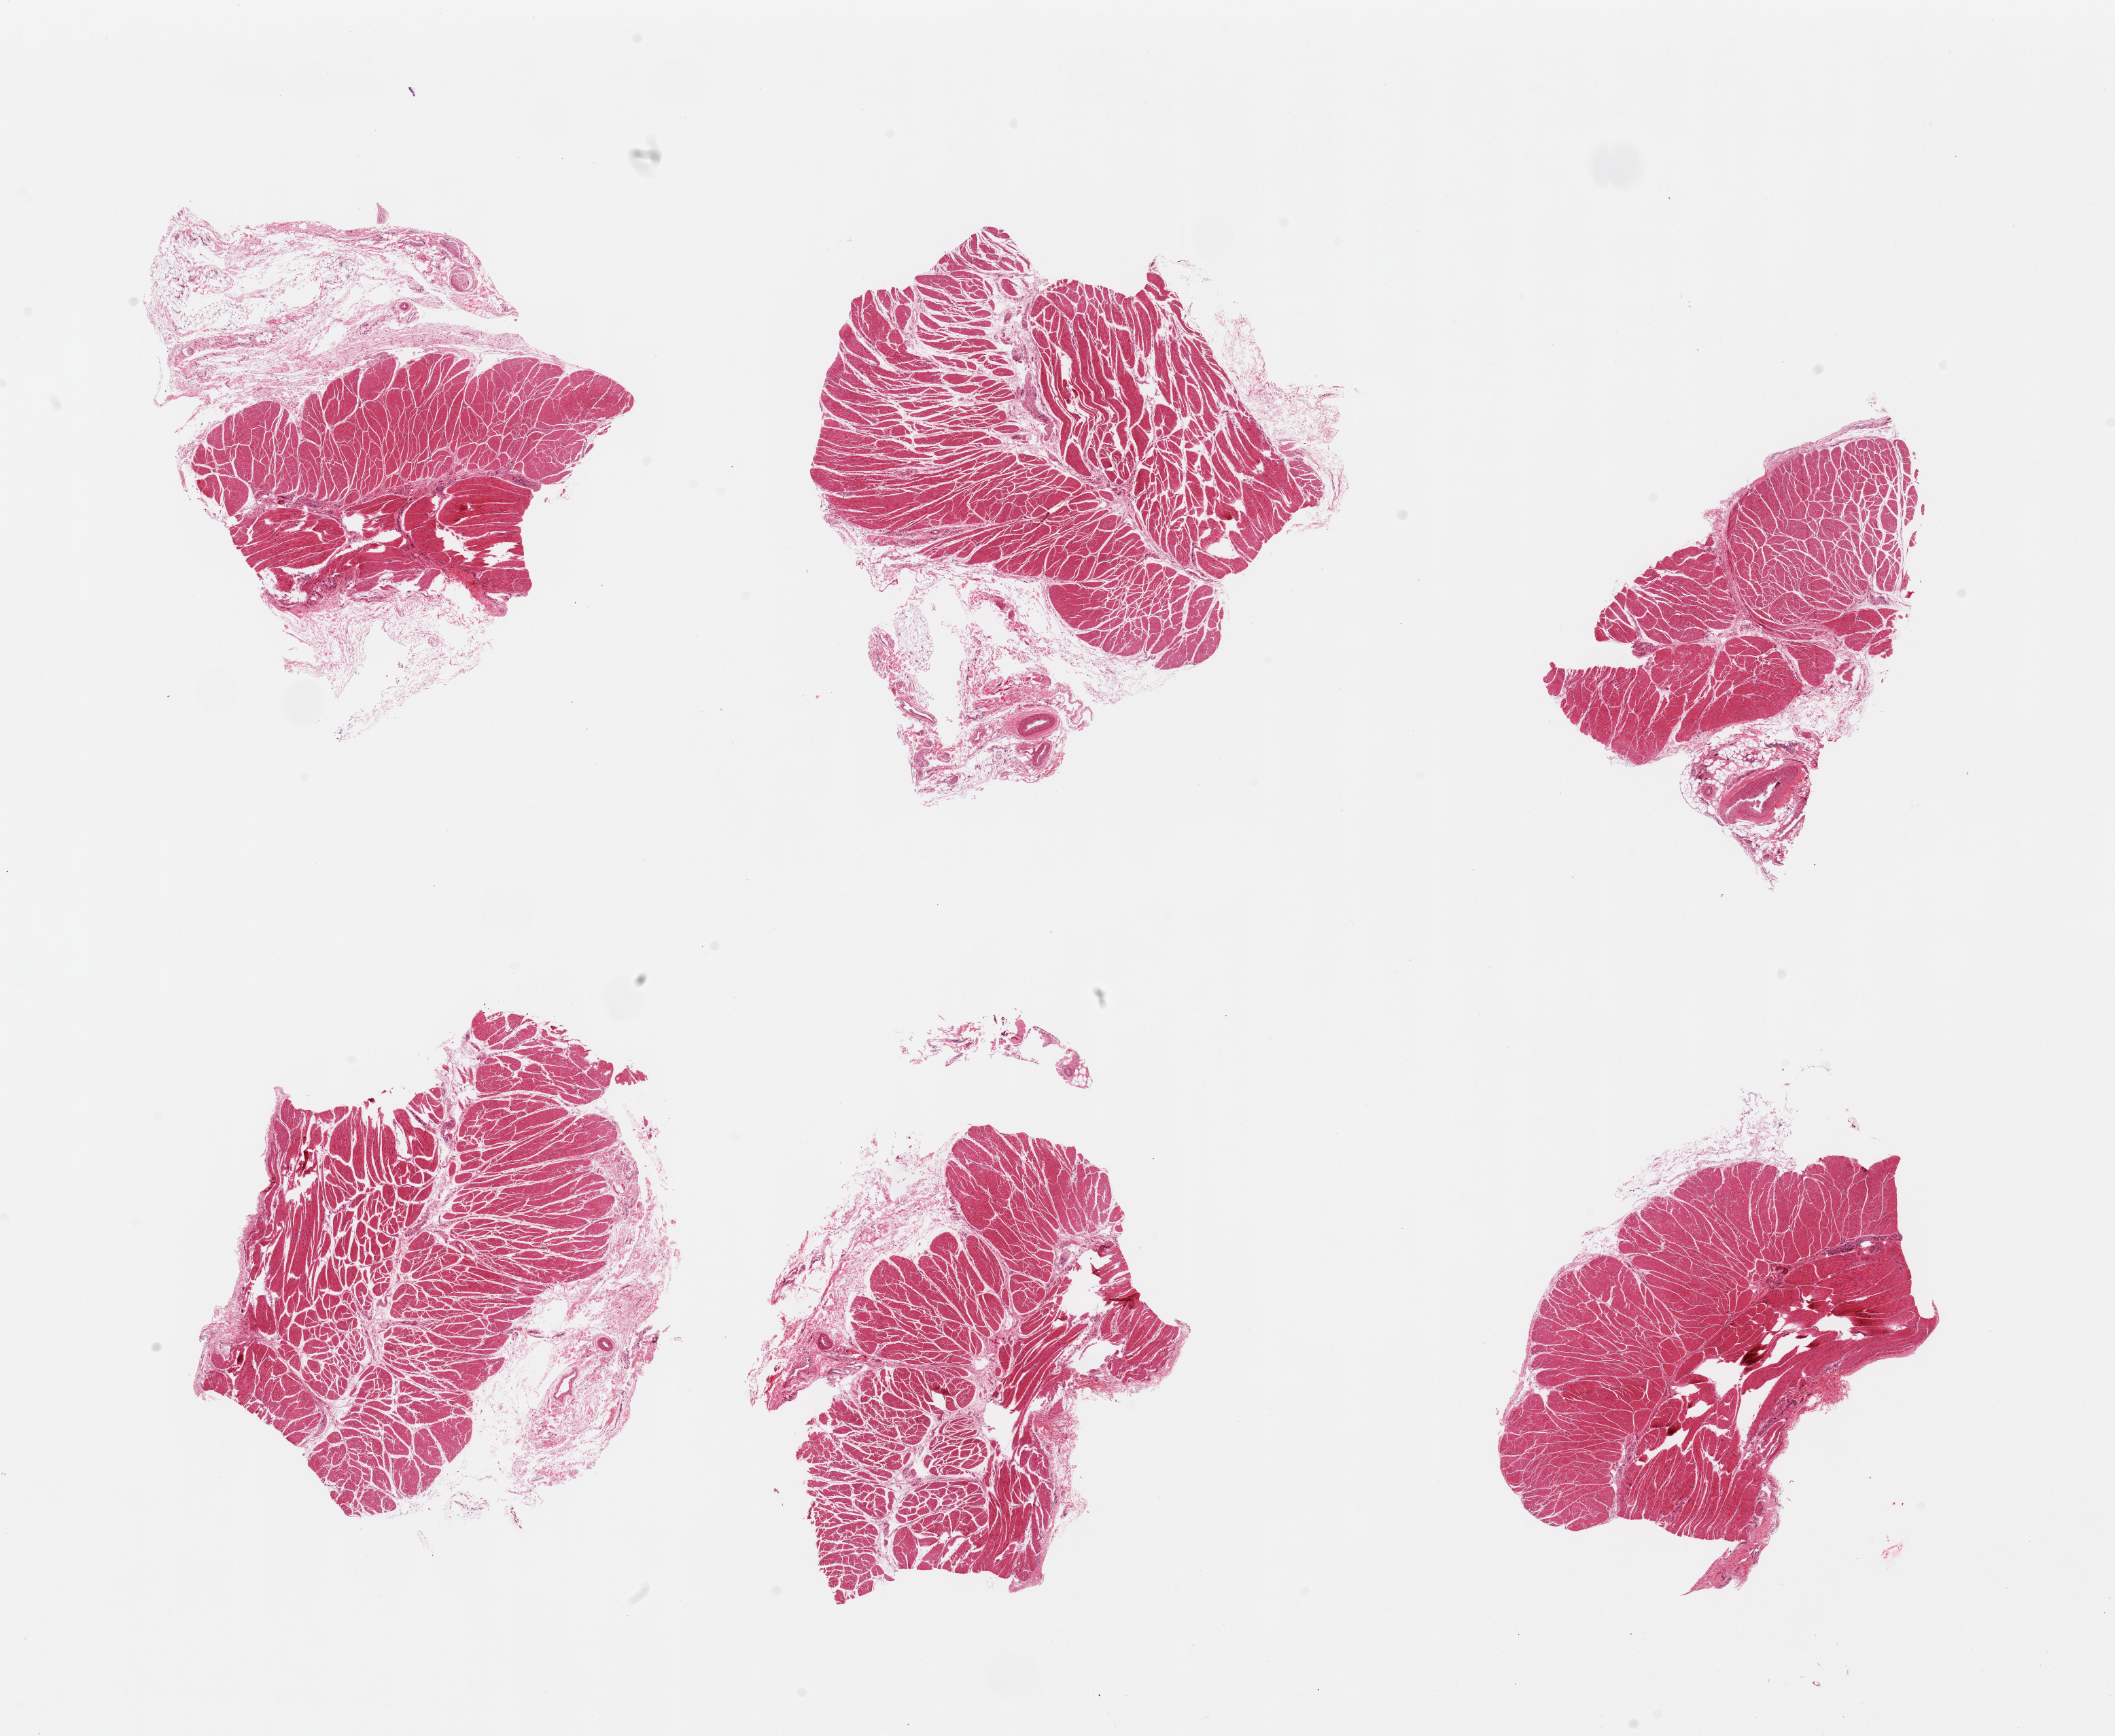
Haematoxylin and eosin whole-slide image, a low-resolution overview of the entire scanned area, about 24.6 x 20.2 mm; PAXgene-fixed paraffin-embedded (PFPE) section; target tissue: esophageal muscle; donor tissue sample. Female donor.
Review note (as recorded): 6 pieces; excessive fibrofatty tissue up to 2 mm thick.